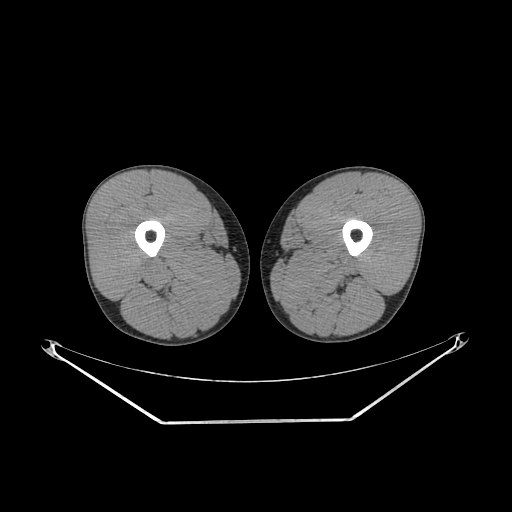
CT of an extremity soft-tissue mass (from a PET/CT study), one axial slice. Slice 224 of 267 in the series (ordered by position). 140 kVp. Soft-tissue window (W 400 / L 40 HU). 3.75 mm slice thickness. 512 × 512 image matrix. Male patient. From the clinical record (not read from this slice): histological type: extraskeletal osteosarcoma; grade: high; site of the primary tumour: left adductur.
Outlined on this slice (expert contour drawn on MRI and transferred to this co-registered scan by the dataset authors):
- gross tumour volume (mass): bounding box (x1, y1, x2, y2) in pixels: (281, 249, 366, 302)